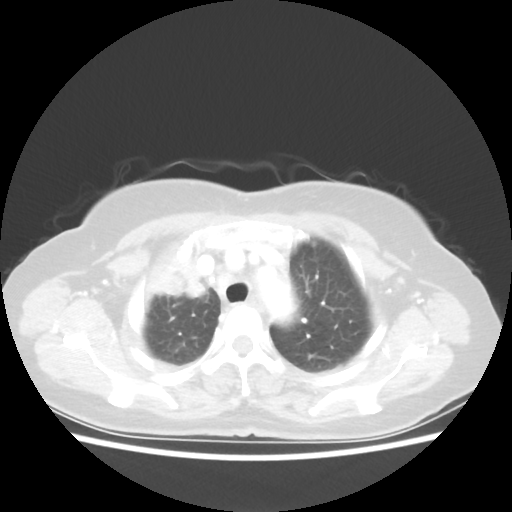
Chest CT, one axial slice; slice 43 of 55 in the series (ordered by position); reconstruction kernel STANDARD; 80 kVp; lung window (W 1500 / L -600 HU); 5 mm slice thickness; 512 × 512 image matrix, field of view 337 × 337 mm. Female patient, age 62 years. Case-level facts recorded for this patient, not image findings: clinical TNM (as recorded): T4 N3 M0.
Structures marked on this image (bounding box drawn by a radiologist):
- lung tumour (recorded histology: squamous cell carcinoma): bounding box [x1, y1, x2, y2] px = [142, 242, 216, 310]